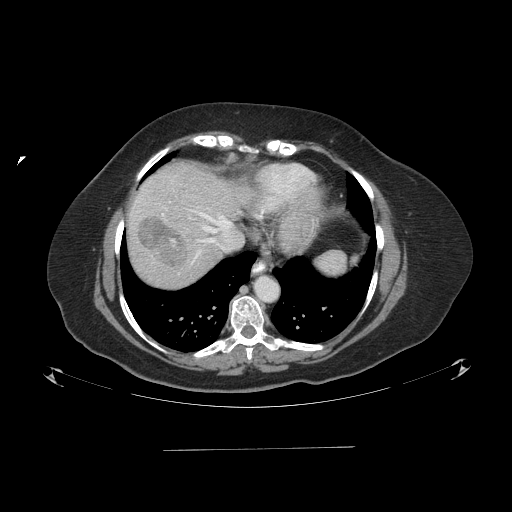
Contrast-enhanced abdominal CT (liver protocol), one axial slice. Slice 78 of 103 in the series (ordered by position). Reconstruction kernel STANDARD. 120 kVp. One of 2 acquisitions stored at this slice position. Soft-tissue window (W 400 / L 40 HU). 512 × 512 image matrix. From the clinical record (not read from this slice): diagnosis: hepatocellular carcinoma (patient treated with transarterial chemoembolisation; whether this scan precedes or follows treatment is not stated here); TNM stage (as recorded): Stage-IIIA; Child-Pugh class: A; tumour size: 5.2 cm.
Structures marked on this image (semi-automatic segmentation, software-assisted and operator-edited):
- liver parenchyma outside the tumour (the mass and vessels are separate outlines, so this box may not span the whole liver): bounding box [x1, y1, x2, y2] px = [128, 162, 256, 288]
- mass: [137, 215, 189, 269]
- liver vessels: [162, 209, 232, 264]